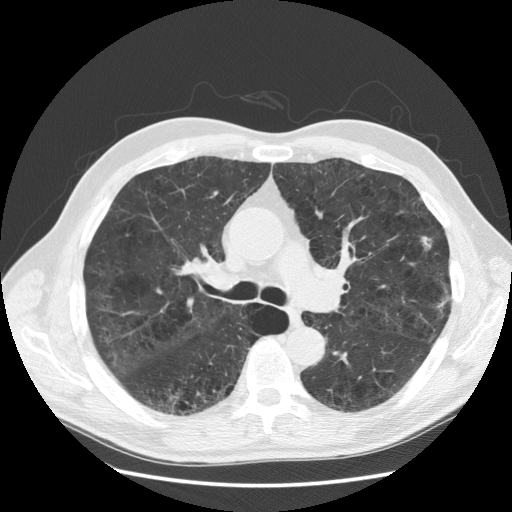
Axial slice from a low-dose chest CT screening exam; third screening round (two years after baseline); lung window (W 1500 / L -600 HU); 2.5 mm slice thickness; slice 68 of 163 in the series; 512 × 512 image matrix, field of view 380 × 380 mm. Male participant, aged 58 years at enrolment. Current smoker at enrolment.
- Expert reader's lesion annotation, box from (x=409, y=224) to (x=446, y=259) px.
- Reader record for this screening exam (exam-level; its link to the box is not recorded): non-calcified nodule or mass ≥4 mm, left upper lobe, 9 × 8 mm, poorly defined margins, soft tissue attenuation, pre-existing on the prior screen: no.
- Lung cancer was diagnosed 53 days after this screen: adenocarcinoma, NOS, left upper lobe, stage IA (AJCC 6th edition), 9 mm at pathology.